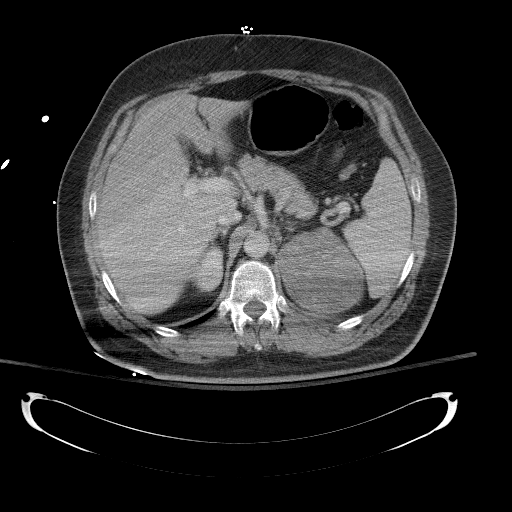
Contrast-enhanced abdominal CT, one axial slice; position 89 of 154 along the scan axis; reconstruction kernel B41f; soft-tissue window (W 400 / L 40 HU); 512 × 512 image matrix, field of view 467 × 467 mm. Male patient, age 43 years. From the clinical record (not read from this slice): diagnosis: adrenocortical carcinoma; tumour side: left adrenal; tumour size at pathology: 9.8 cm; Ki-67 index: 30 %; stage (as recorded): 2.
Structures marked on this image (semi-automatically segmented with operator editing):
- mass: bounding box (x1, y1, x2, y2) in pixels: (279, 228, 361, 311)